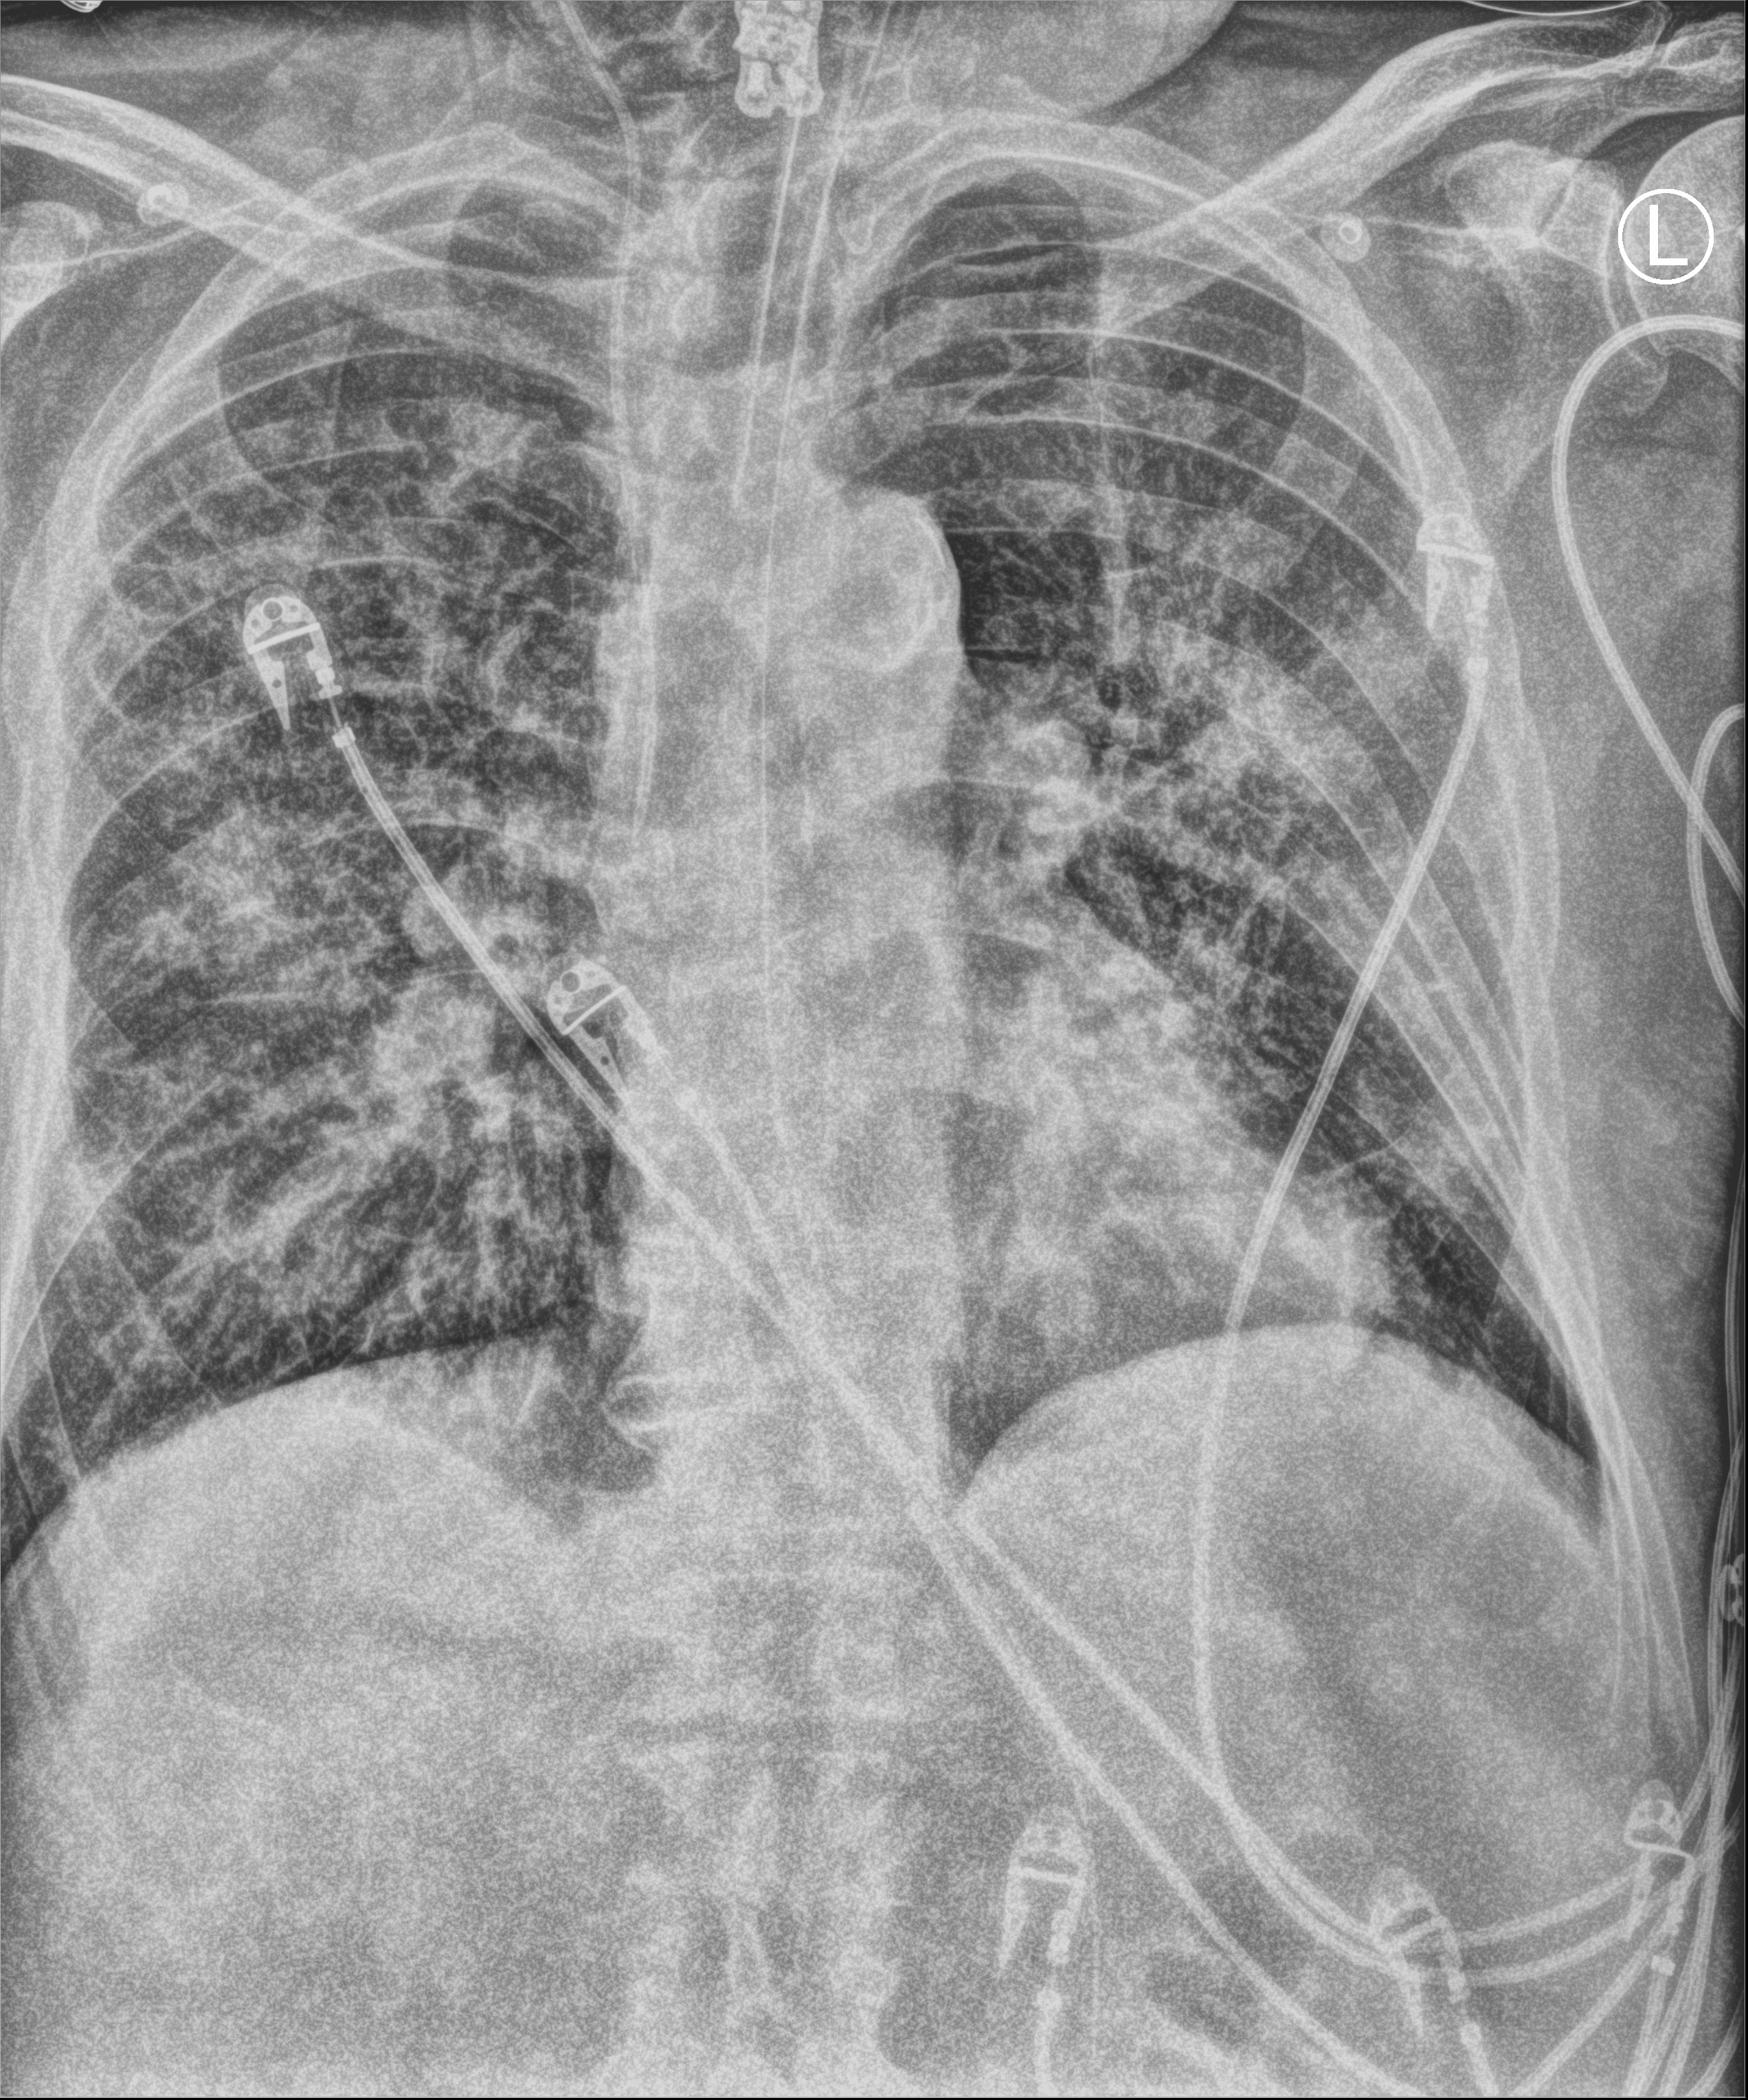
Chest X-ray (portable); anteroposterior (AP) projection. Male patient hospitalised with COVID-19, age 75–90 years.
From the hospital-stay record, not from the radiograph (when in the stay this image was taken is not recorded):
- admitted to intensive care during this hospital stay: yes
- mechanically ventilated during this hospital stay: yes